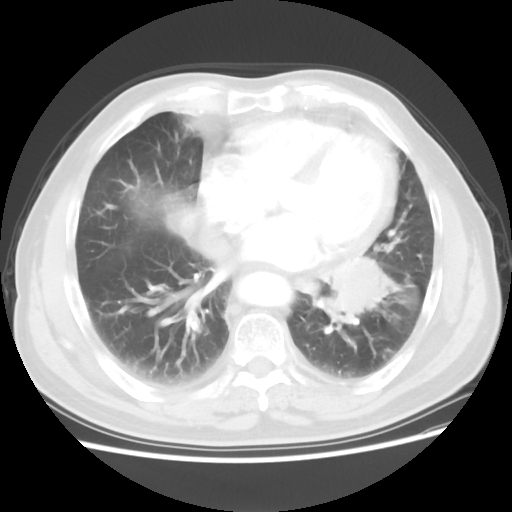
Chest CT, one axial slice; slice 24 of 56 in the series (ordered by position); reconstruction kernel STANDARD; 120 kVp; lung window (W 1500 / L -600 HU); 5 mm slice thickness; 512 × 512 image matrix. Patient: male, 75 years. From the clinical record (not read from this slice): clinical TNM (as recorded): T3 N0 M0.
Structures marked on this image (rectangle marked by the reading radiologist):
- lung tumour (recorded histology: squamous cell carcinoma): bounding box <325,259,393,325> (left, top, right, bottom; pixels)